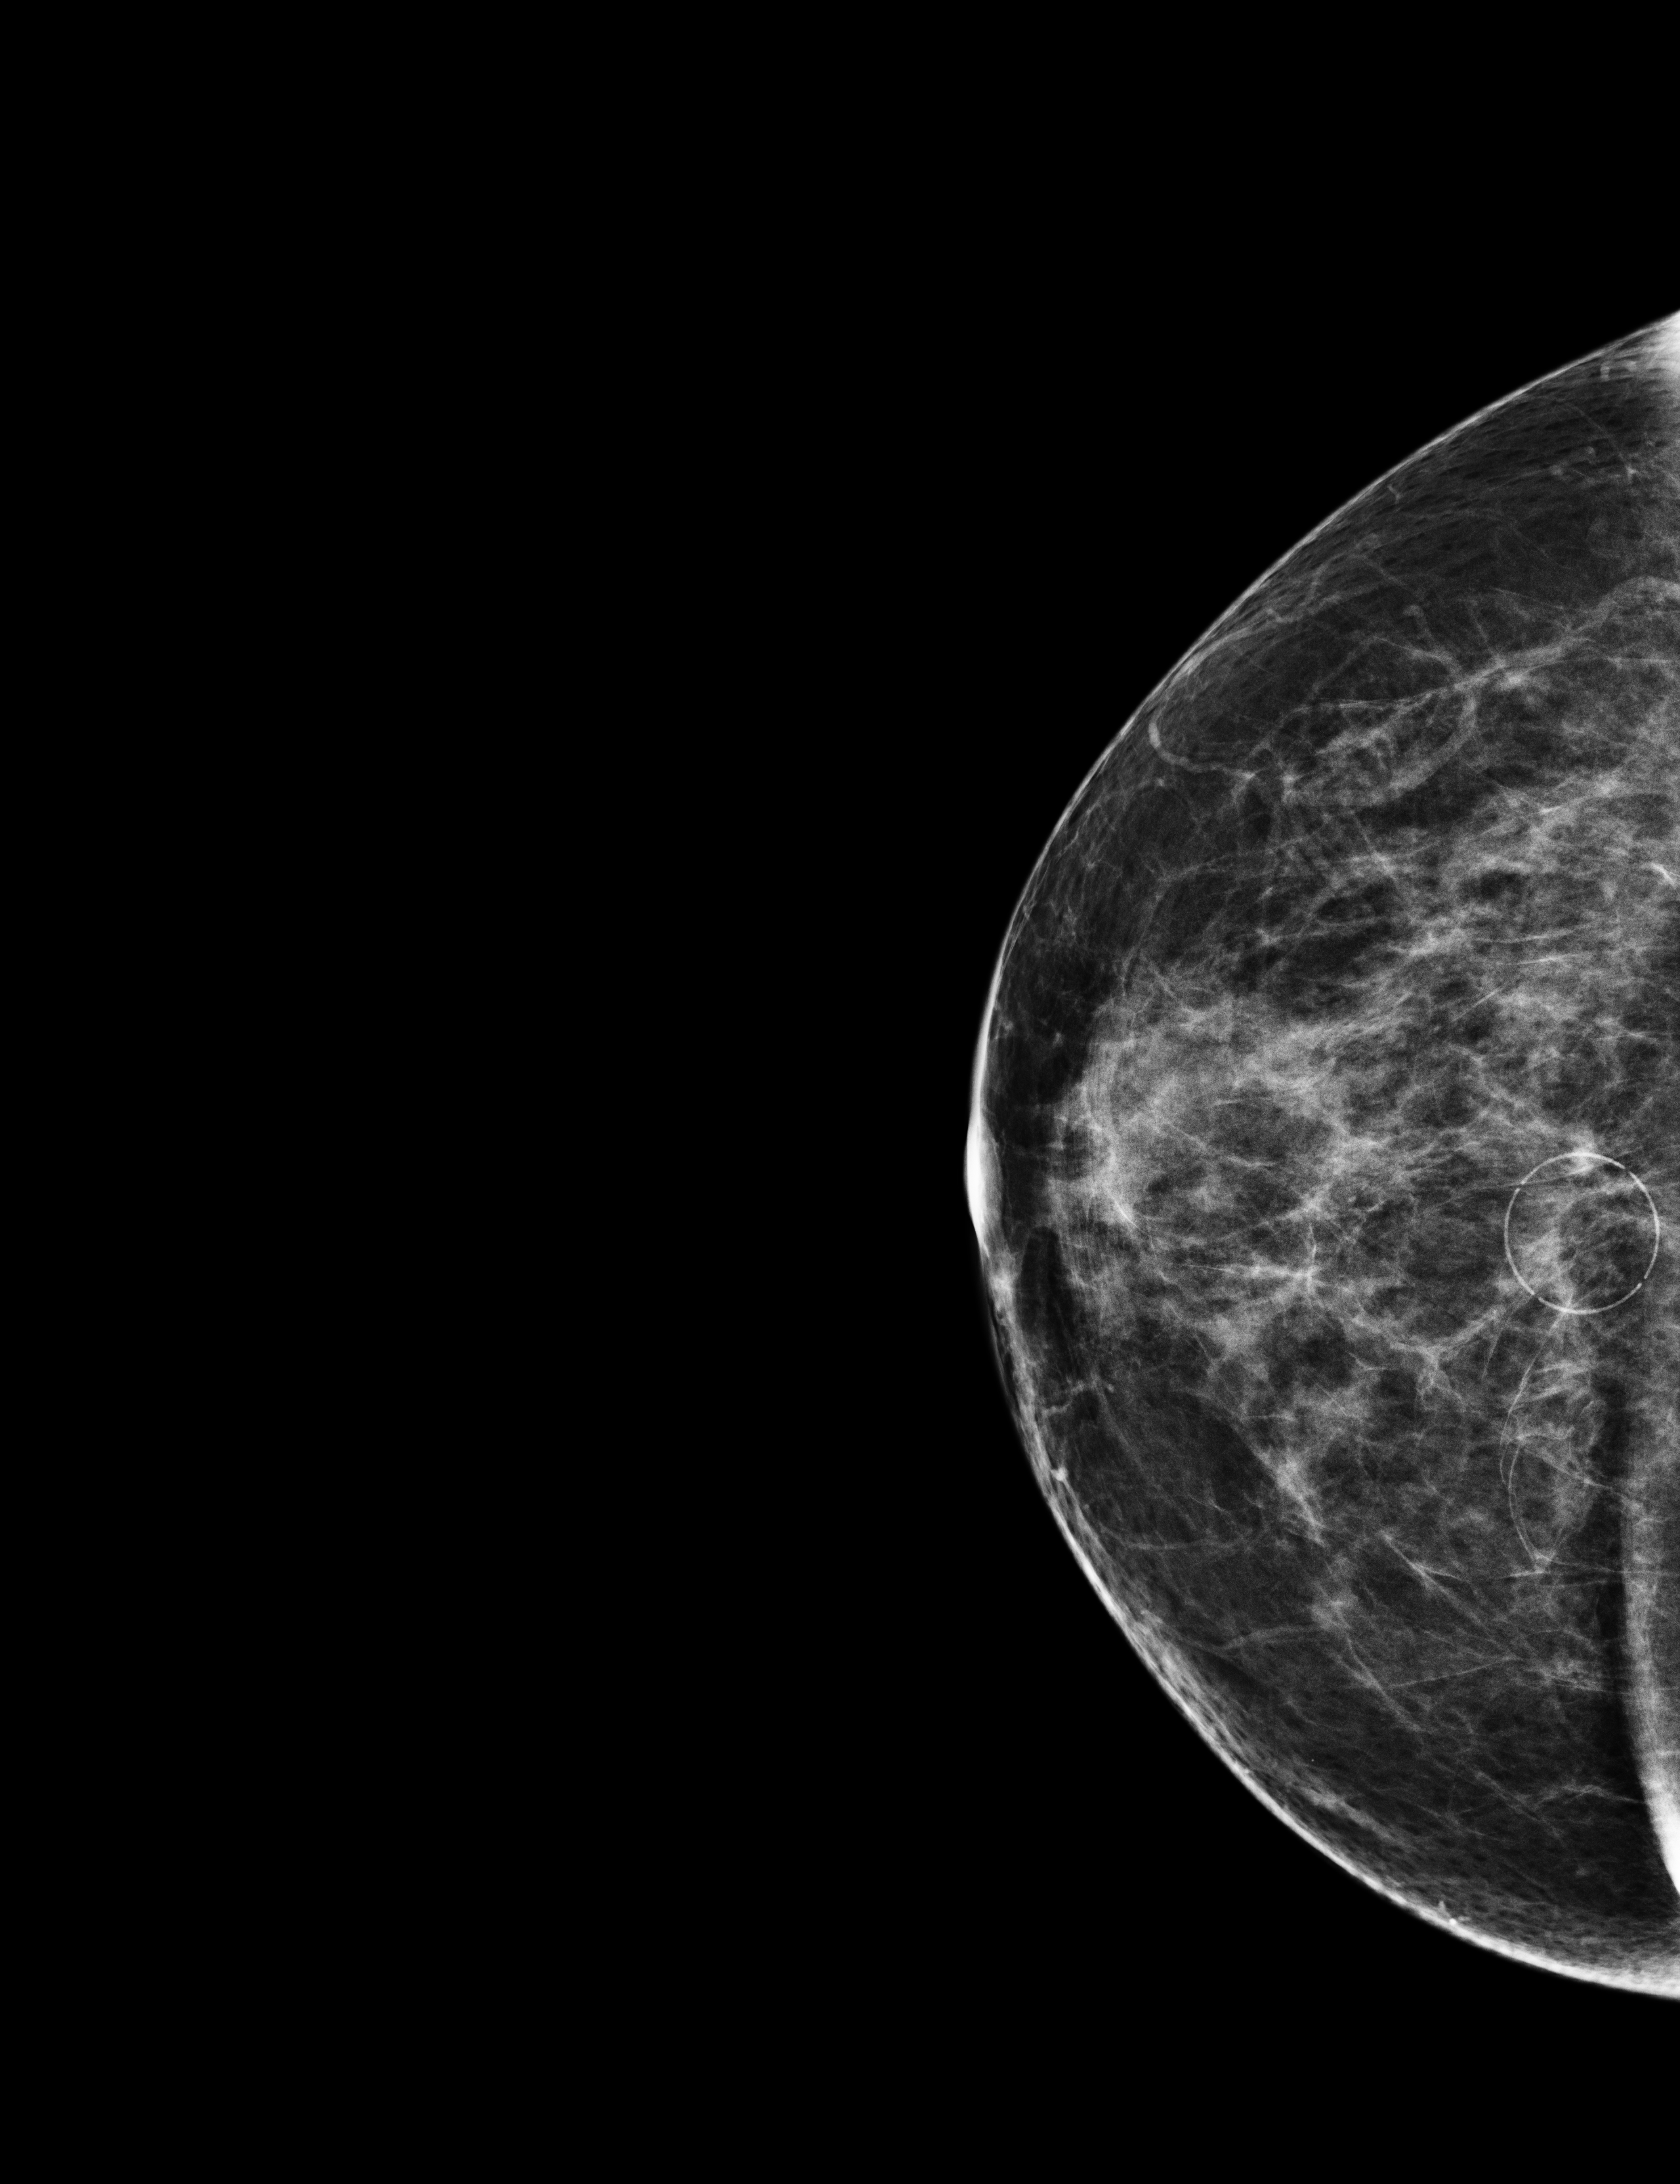
Annual screening mammography examination. Patient: female, 61 years.
Image type: full-field digital mammogram. Breast: right. Projection: CC view.